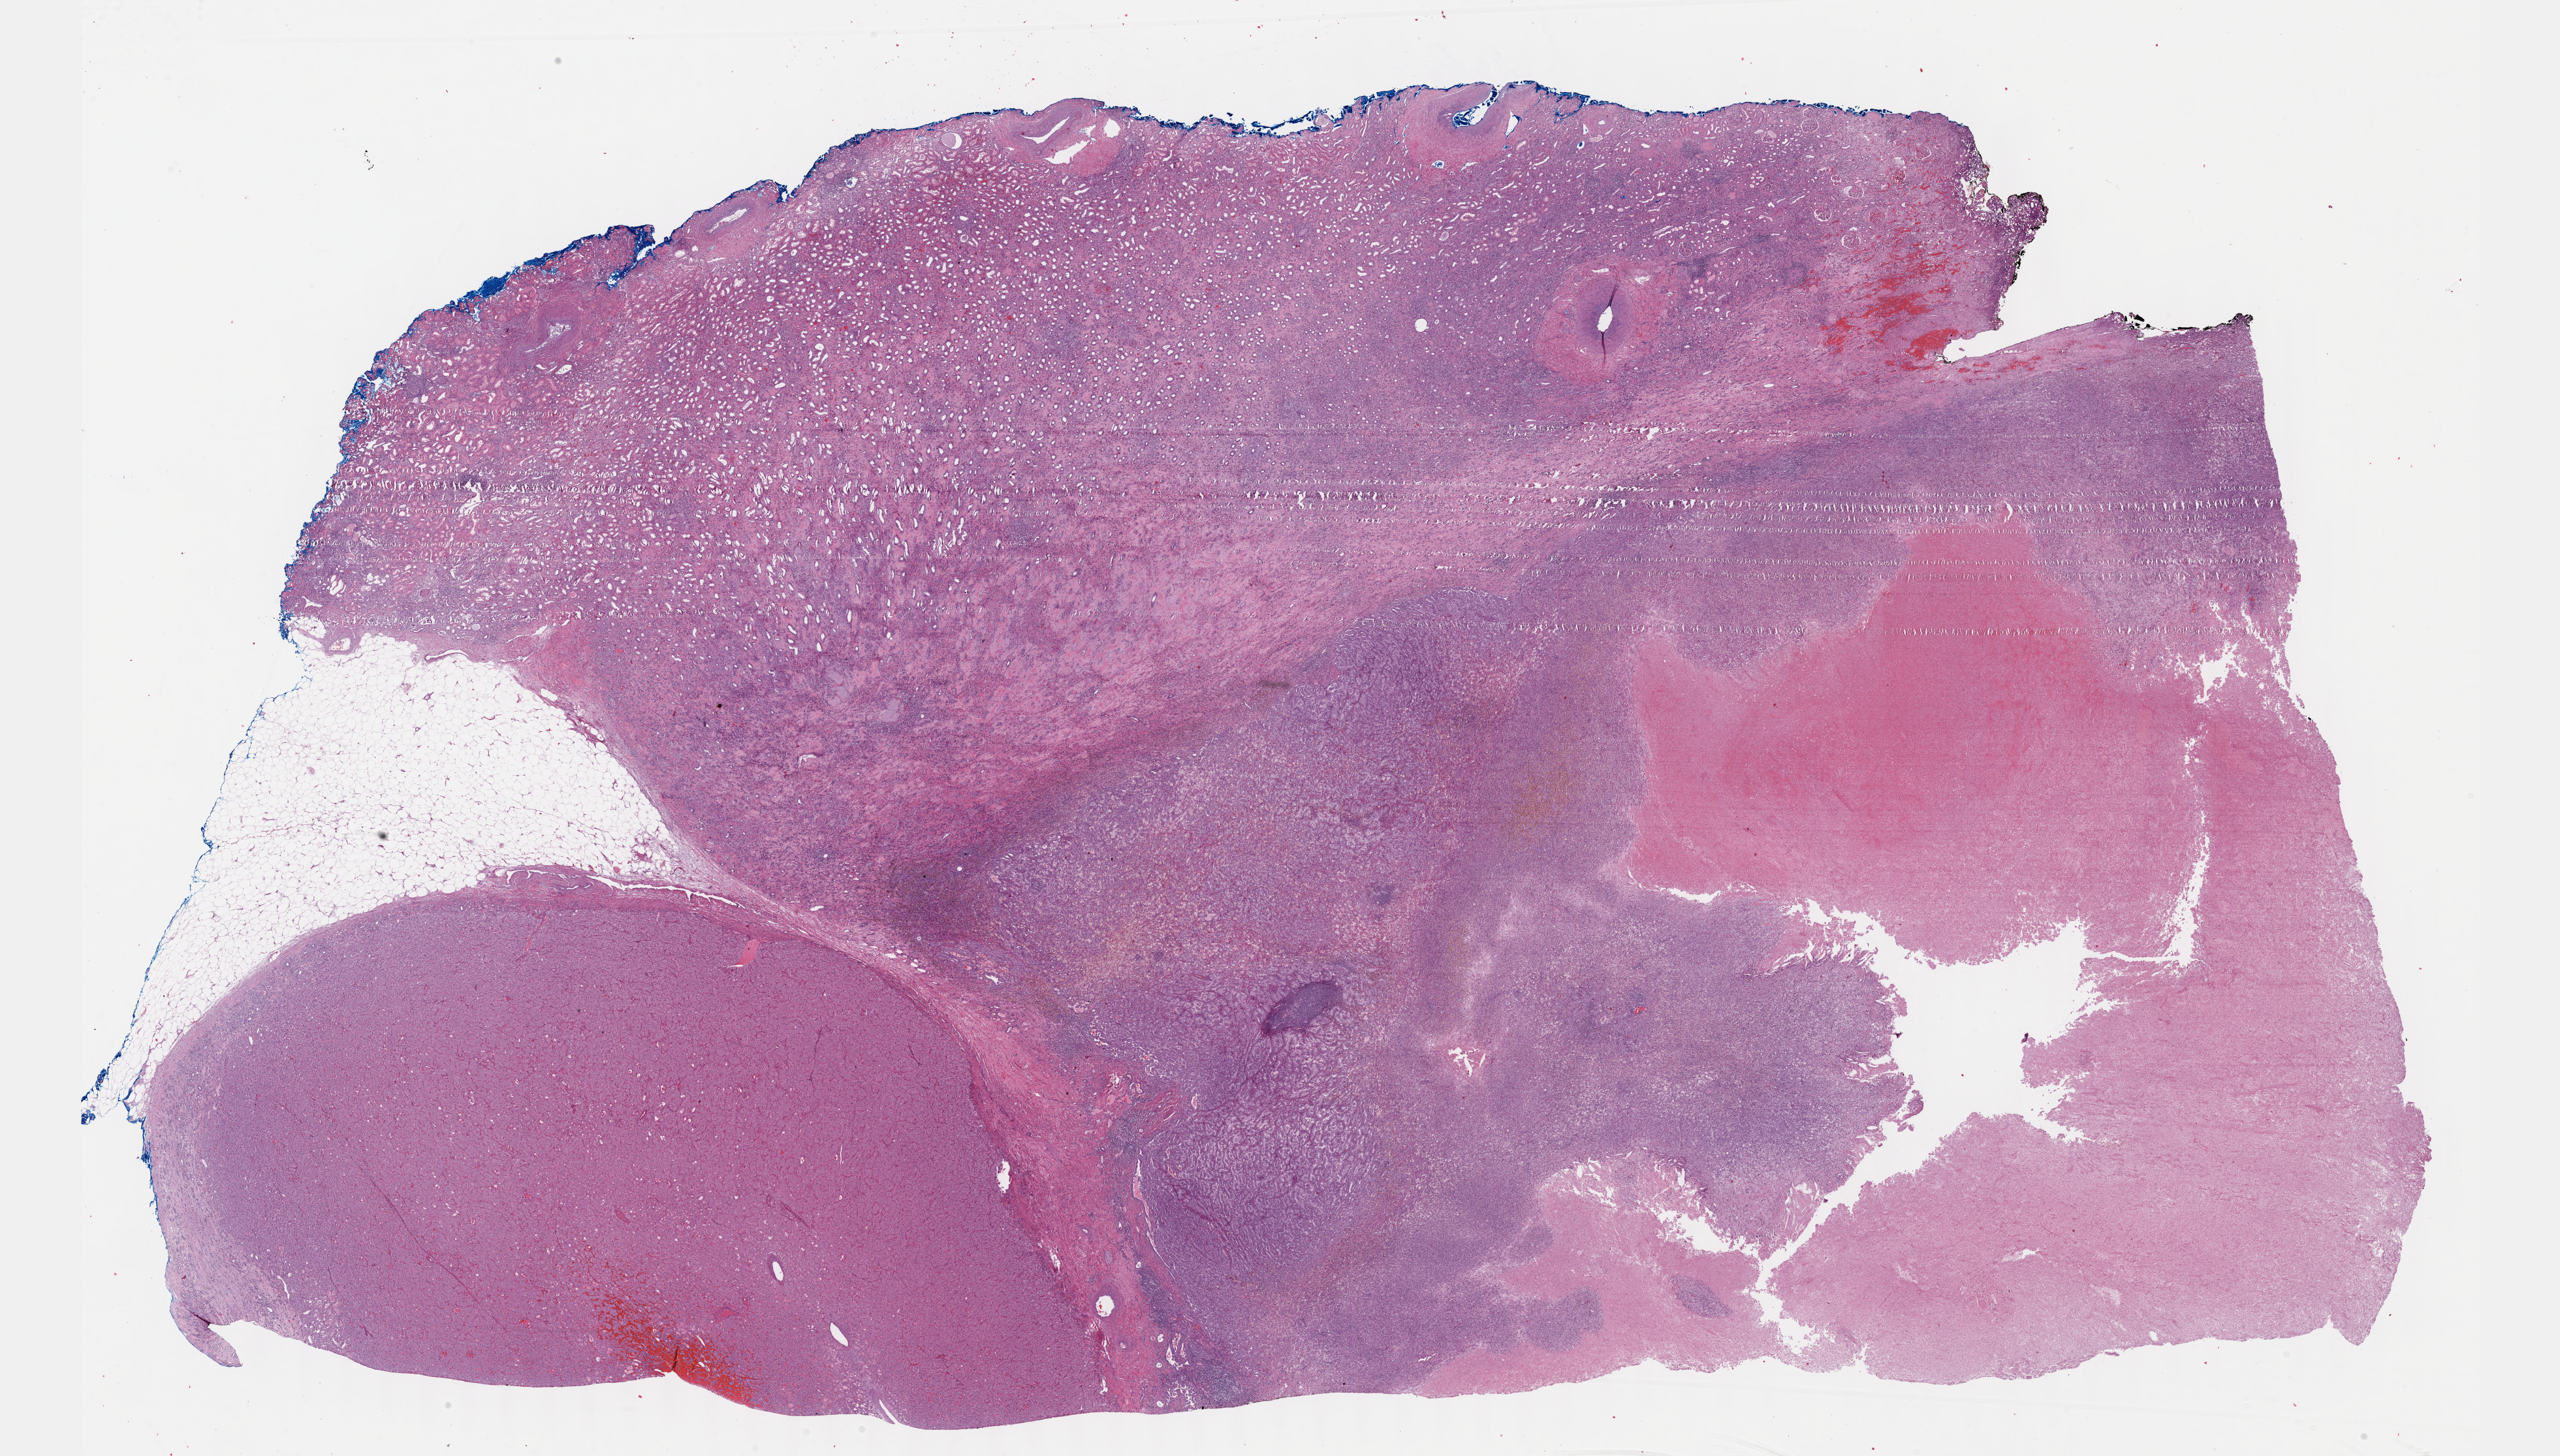
H&E-stained whole-slide image, shown as a low-resolution overview of the whole scanned area (about 31.7 x 18.0 mm, slide scanned at 40x). Formalin-fixed paraffin-embedded (FFPE) diagnostic section. Sample: primary tumour, kidney. Patient: male, age at initial diagnosis 63 years.
AJCC pathologic stage: I. Histologic diagnosis: Papillary adenocarcinoma, NOS.